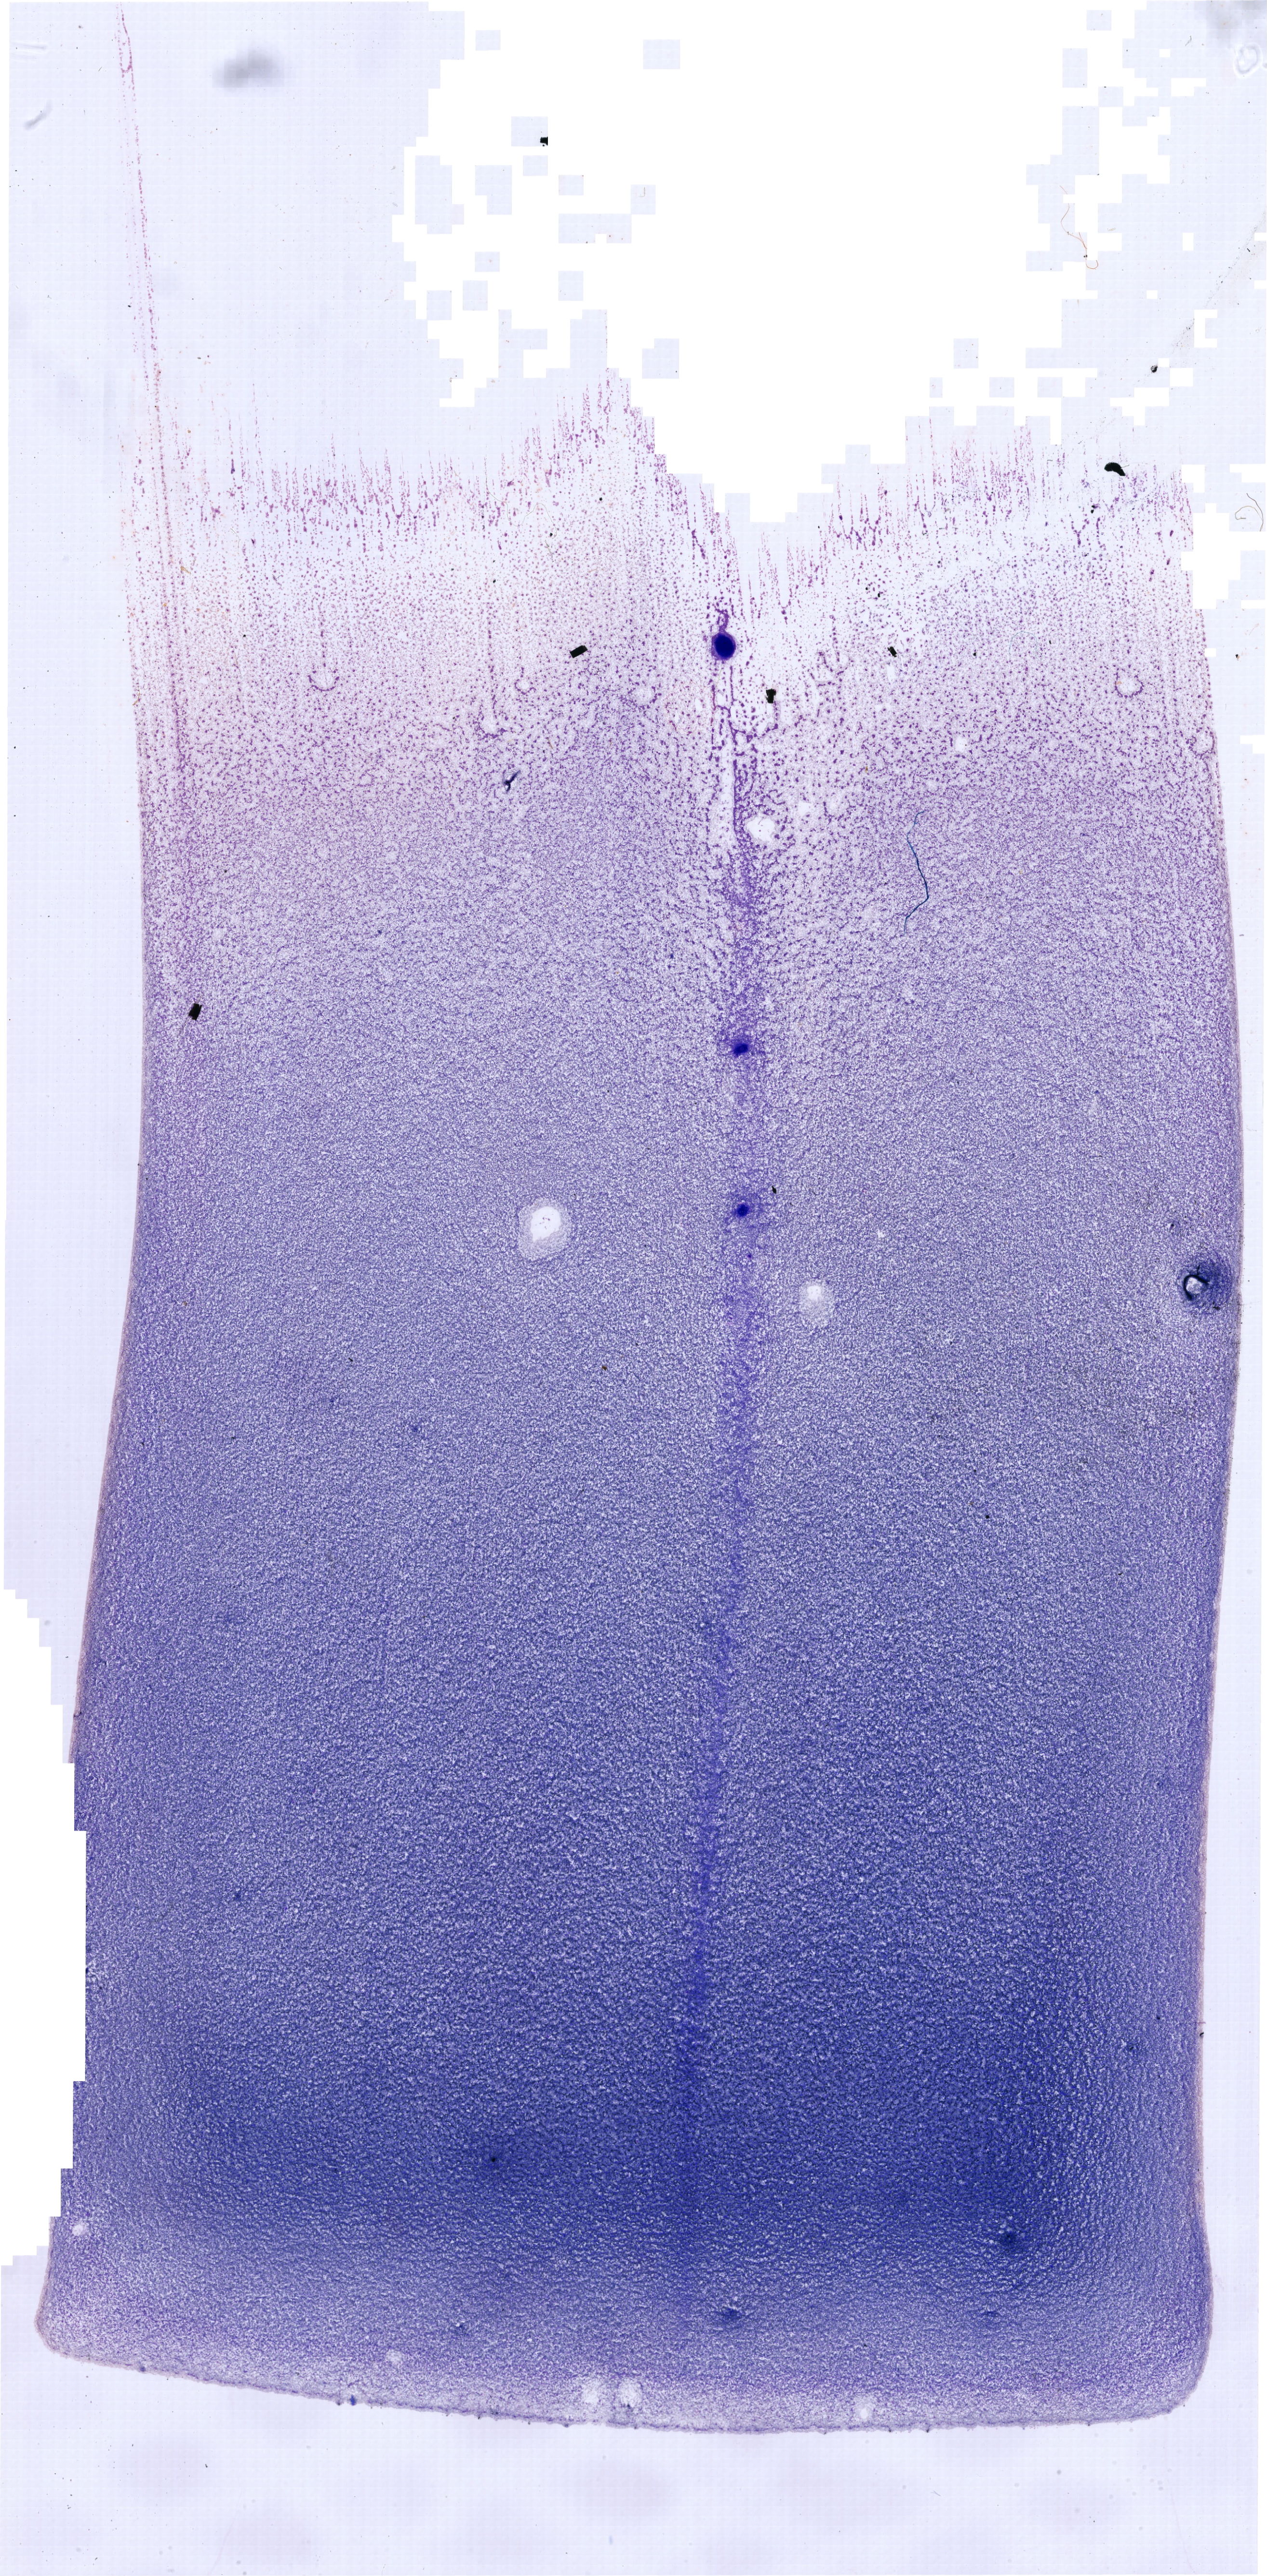
May-Grünwald–Giemsa-stained marrow aspirate smear (whole slide), whole scanned area (about 20.5 x 41.7 mm) shown as a low-resolution overview. Male patient.
- diagnosis: Mixed Phenotype Acute Leukemia, B/Myeloid